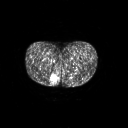
FDG PET of an extremity soft-tissue mass (from a PET/CT study), one axial slice; slice 17 of 267 in the series (ordered by position); 3.27 mm slice thickness; 128 × 128 image matrix, field of view 700 × 700 mm. Patient: female, 17 years. From the clinical record (not read from this slice): histological type: epithelioid sarcoma; grade: intermediate; site of the primary tumour: right buttock.
Annotated regions visible in this slice (expert contour drawn on MRI and transferred to this co-registered scan by the dataset authors):
- gross tumour volume including surrounding oedema: bounding box <50,74,60,87> (left, top, right, bottom; pixels)
- gross tumour volume (mass): <51,76,56,80>